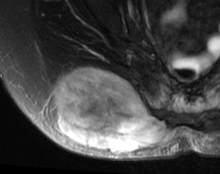
MRI of an extremity soft-tissue mass, one axial slice. Position 31 of 63 along the scan axis. T2-weighted fat-saturated. MR volume resampled by the dataset authors to the PET/CT grid (not the native acquisition matrix). 3.27 mm slice thickness. 220 × 174 image matrix, field of view 215 × 170 mm. Female patient. Case-level facts recorded for this patient, not image findings: histological type: spindle cell suggestive of myxofibrosarcoma; grade: intermediate; site of the primary tumour: right buttock.
Annotated regions visible in this slice (expert contour drawn on MRI and transferred to this co-registered scan by the dataset authors):
- gross tumour volume (mass): box from (x=54, y=68) to (x=180, y=154) px